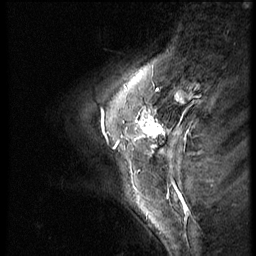
Breast MRI (dynamic contrast-enhanced), one sagittal slice; dynamic contrast-enhanced series, image 2 of 3 at this slice position (ordered by acquisition); 1.5 T; TE 4.2 ms, TR 9 ms; 256 × 256 image matrix, field of view 180 × 180 mm. Patient: female, 46 years. From the clinical record (not read from this slice): setting: breast cancer imaged before/during neoadjuvant chemotherapy; receptor status: HER2-positive.
Annotated regions visible in this slice (semi-automatic segmentation, software-assisted and operator-edited):
- analysis volume of interest (the breast-tissue region the enhancement analysis was run in; not a lesion): box from (x=71, y=98) to (x=174, y=182) px
- tumour enhancement mask (voxels above the 140 % enhancement threshold inside the analysis volume of interest): (x=103, y=110)–(x=165, y=147)